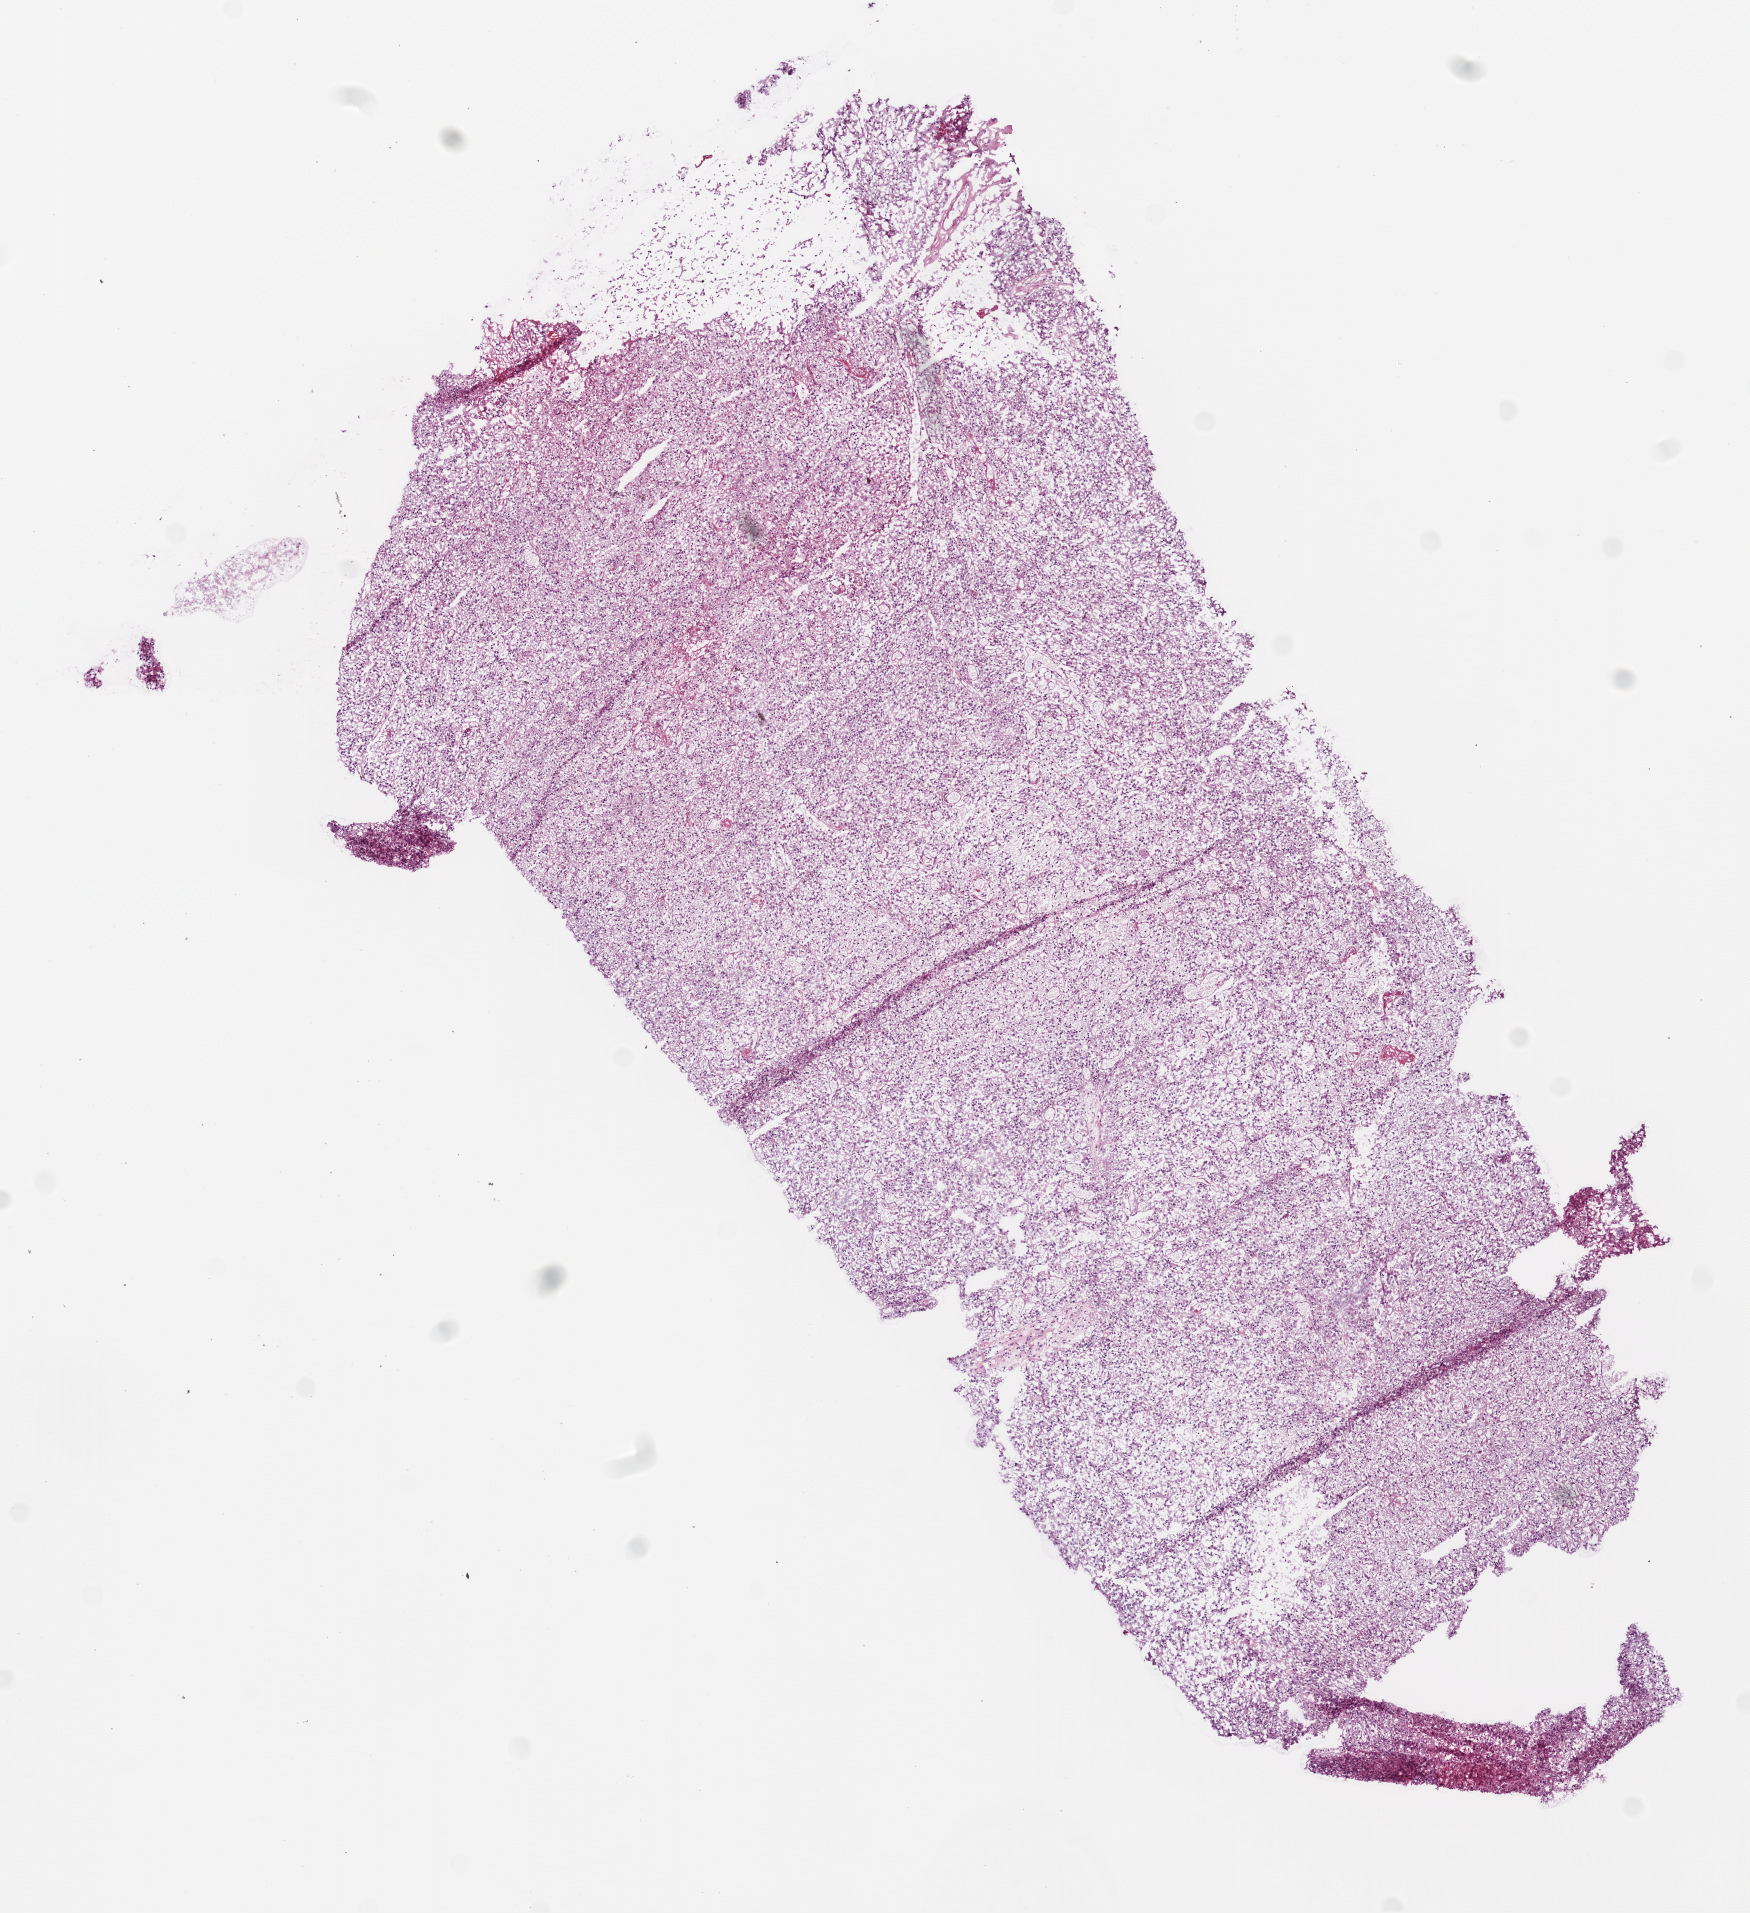
Whole-slide histology image, Hematoxylin and eosin (H&E) stained, whole scanned area (about 7.0 x 7.7 mm) shown as a low-resolution overview; frozen section from the top of the tissue portion; brain, primary tumour sample. Patient: female, age at initial diagnosis 76 years. Pathologist review of this section (percent, as recorded): tumour cells 90%, tumour nuclei 90%, normal cells 0%, stromal cells 5%, necrosis 5%.
• histologic diagnosis: Glioblastoma